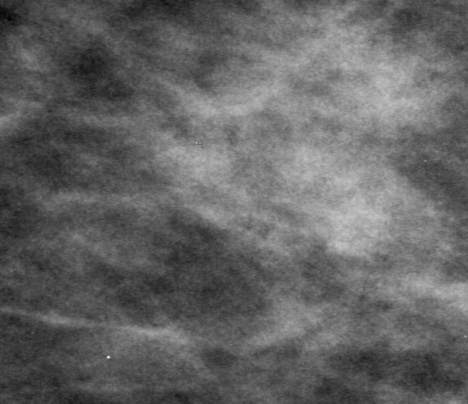
Region of interest cut from a scanned film mammogram (one marked finding), left breast, MLO view, BI-RADS breast density category 2 (scale 1–4).
Marked abnormality: mass, shape irregular, margins spiculated; BI-RADS assessment category 3; subtlety rating 2 on a 1 (subtle) to 5 (obvious) scale; pathology (as recorded): malignant.